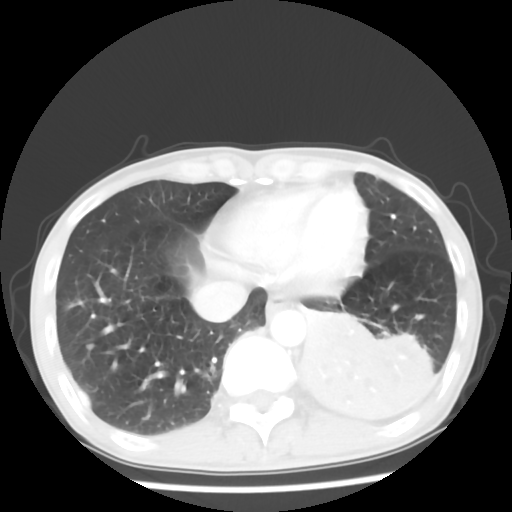
Chest CT, one axial slice. Position 16 of 64 along the scan axis. 120 kVp. Lung window (W 1500 / L -600 HU). 5 mm slice thickness. 512 × 512 image matrix. Male patient, age 68 years. Case-level facts recorded for this patient, not image findings: clinical TNM (as recorded): T4 N0 M0.
Structures marked on this image (rectangle marked by the reading radiologist):
- lung tumour (recorded histology: squamous cell carcinoma): bounding box (x1, y1, x2, y2) in pixels: (285, 295, 440, 428)